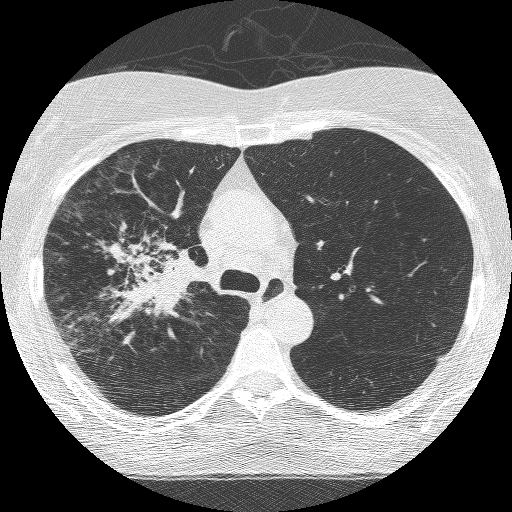
Low-dose screening chest CT, axial slice, third screening round (two years after baseline), lung window (W 1500 / L -600 HU), 1.25 mm slice thickness, 120 kVp. Female, age 64 years at enrolment. Former smoker at enrolment.
Lesion marked by an expert reader, box from (x=91, y=224) to (x=205, y=338) px. The exam's reader record, not a measurement of the box and not confirmed to be the same lesion: non-calcified nodule or mass ≥4 mm, right upper lobe, 49 × 43 mm, spiculated (stellate) margins, soft tissue attenuation, pre-existing on the prior screen: yes; interval growth: yes. Lung cancer was diagnosed 7 days after this screen: adenocarcinoma, NOS, right upper lobe, right middle lobe, right hilum, stage IV (AJCC 6th edition), 85 mm at pathology.